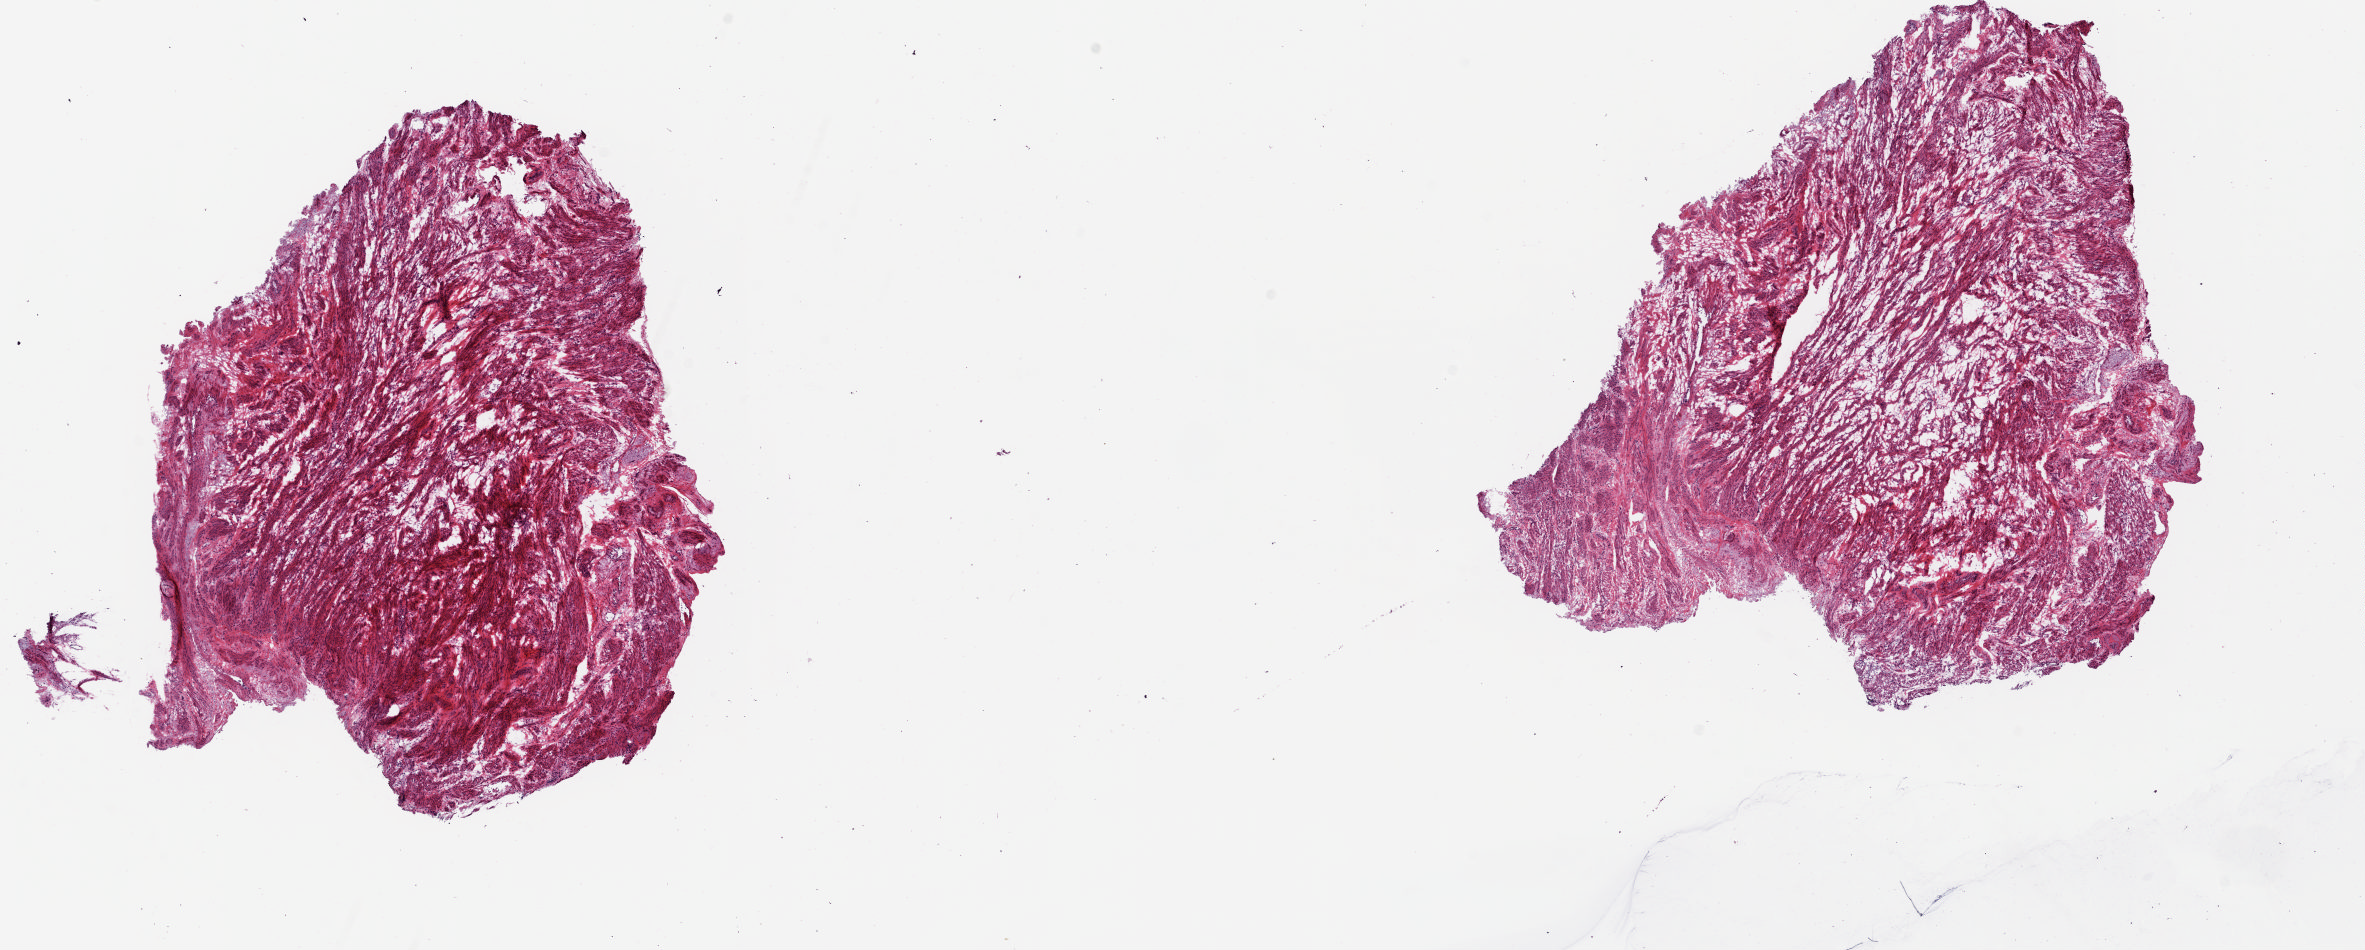
Digitized H&E-stained tissue section (whole slide) — a low-resolution overview of the entire scanned area, about 18.8 x 7.5 mm; frozen section from the top of the tissue portion; solid tissue normal (non-tumour tissue) sample from the uterus. Patient: female, age at initial diagnosis 68 years. Slide review estimates, as recorded: tumour cells 0%, tumour nuclei 0%, normal cells 100%, stromal cells 0%, necrosis 0%. Inflammatory infiltration, as recorded: lymphocyte infiltration 40%, monocyte infiltration 10%, neutrophil infiltration 40%.
* this section: solid tissue normal sample (biorepository sample class)
* patient diagnosis: Endometrioid adenocarcinoma, NOS (endometrium)